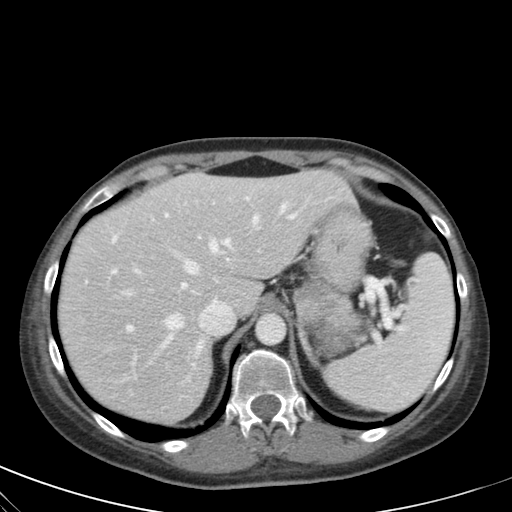
Contrast-enhanced abdominal CT, one axial slice. Slice 46 of 59 in the series (ordered by position). Intravenous contrast given. Soft-tissue window (W 400 / L 40 HU). 4 mm slice thickness. 512 × 512 image matrix, field of view 350 × 350 mm. Female patient, age 28 years. From the clinical record (not read from this slice): diagnosis: adrenocortical carcinoma; tumour side: left adrenal; tumour size at pathology: 7 cm; Ki-67 index: 40 %; stage (as recorded): 4.
Structures marked on this image (semi-automatic segmentation, software-assisted and operator-edited):
- mass: bounding box [x1, y1, x2, y2] px = [295, 282, 367, 355]